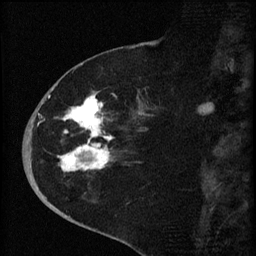
Breast MRI (dynamic contrast-enhanced), one sagittal slice; slice 28 of 60 in the series (ordered by position); dynamic contrast-enhanced series, image 2 of 4 at this slice position (ordered by acquisition); 1.5 T; TE 4.2 ms, TR 8.2 ms; 2 mm slice thickness; 256 × 256 image matrix, field of view 180 × 180 mm. Patient: female, 71 years.
Annotated regions visible in this slice (semi-automatic segmentation, software-assisted and operator-edited):
- analysis volume of interest (the breast-tissue region the enhancement analysis was run in; not a lesion): bounding box <35,75,153,190> (left, top, right, bottom; pixels)
- tumour enhancement mask (voxels above the 70 % enhancement threshold inside the analysis volume of interest): <53,85,114,172>